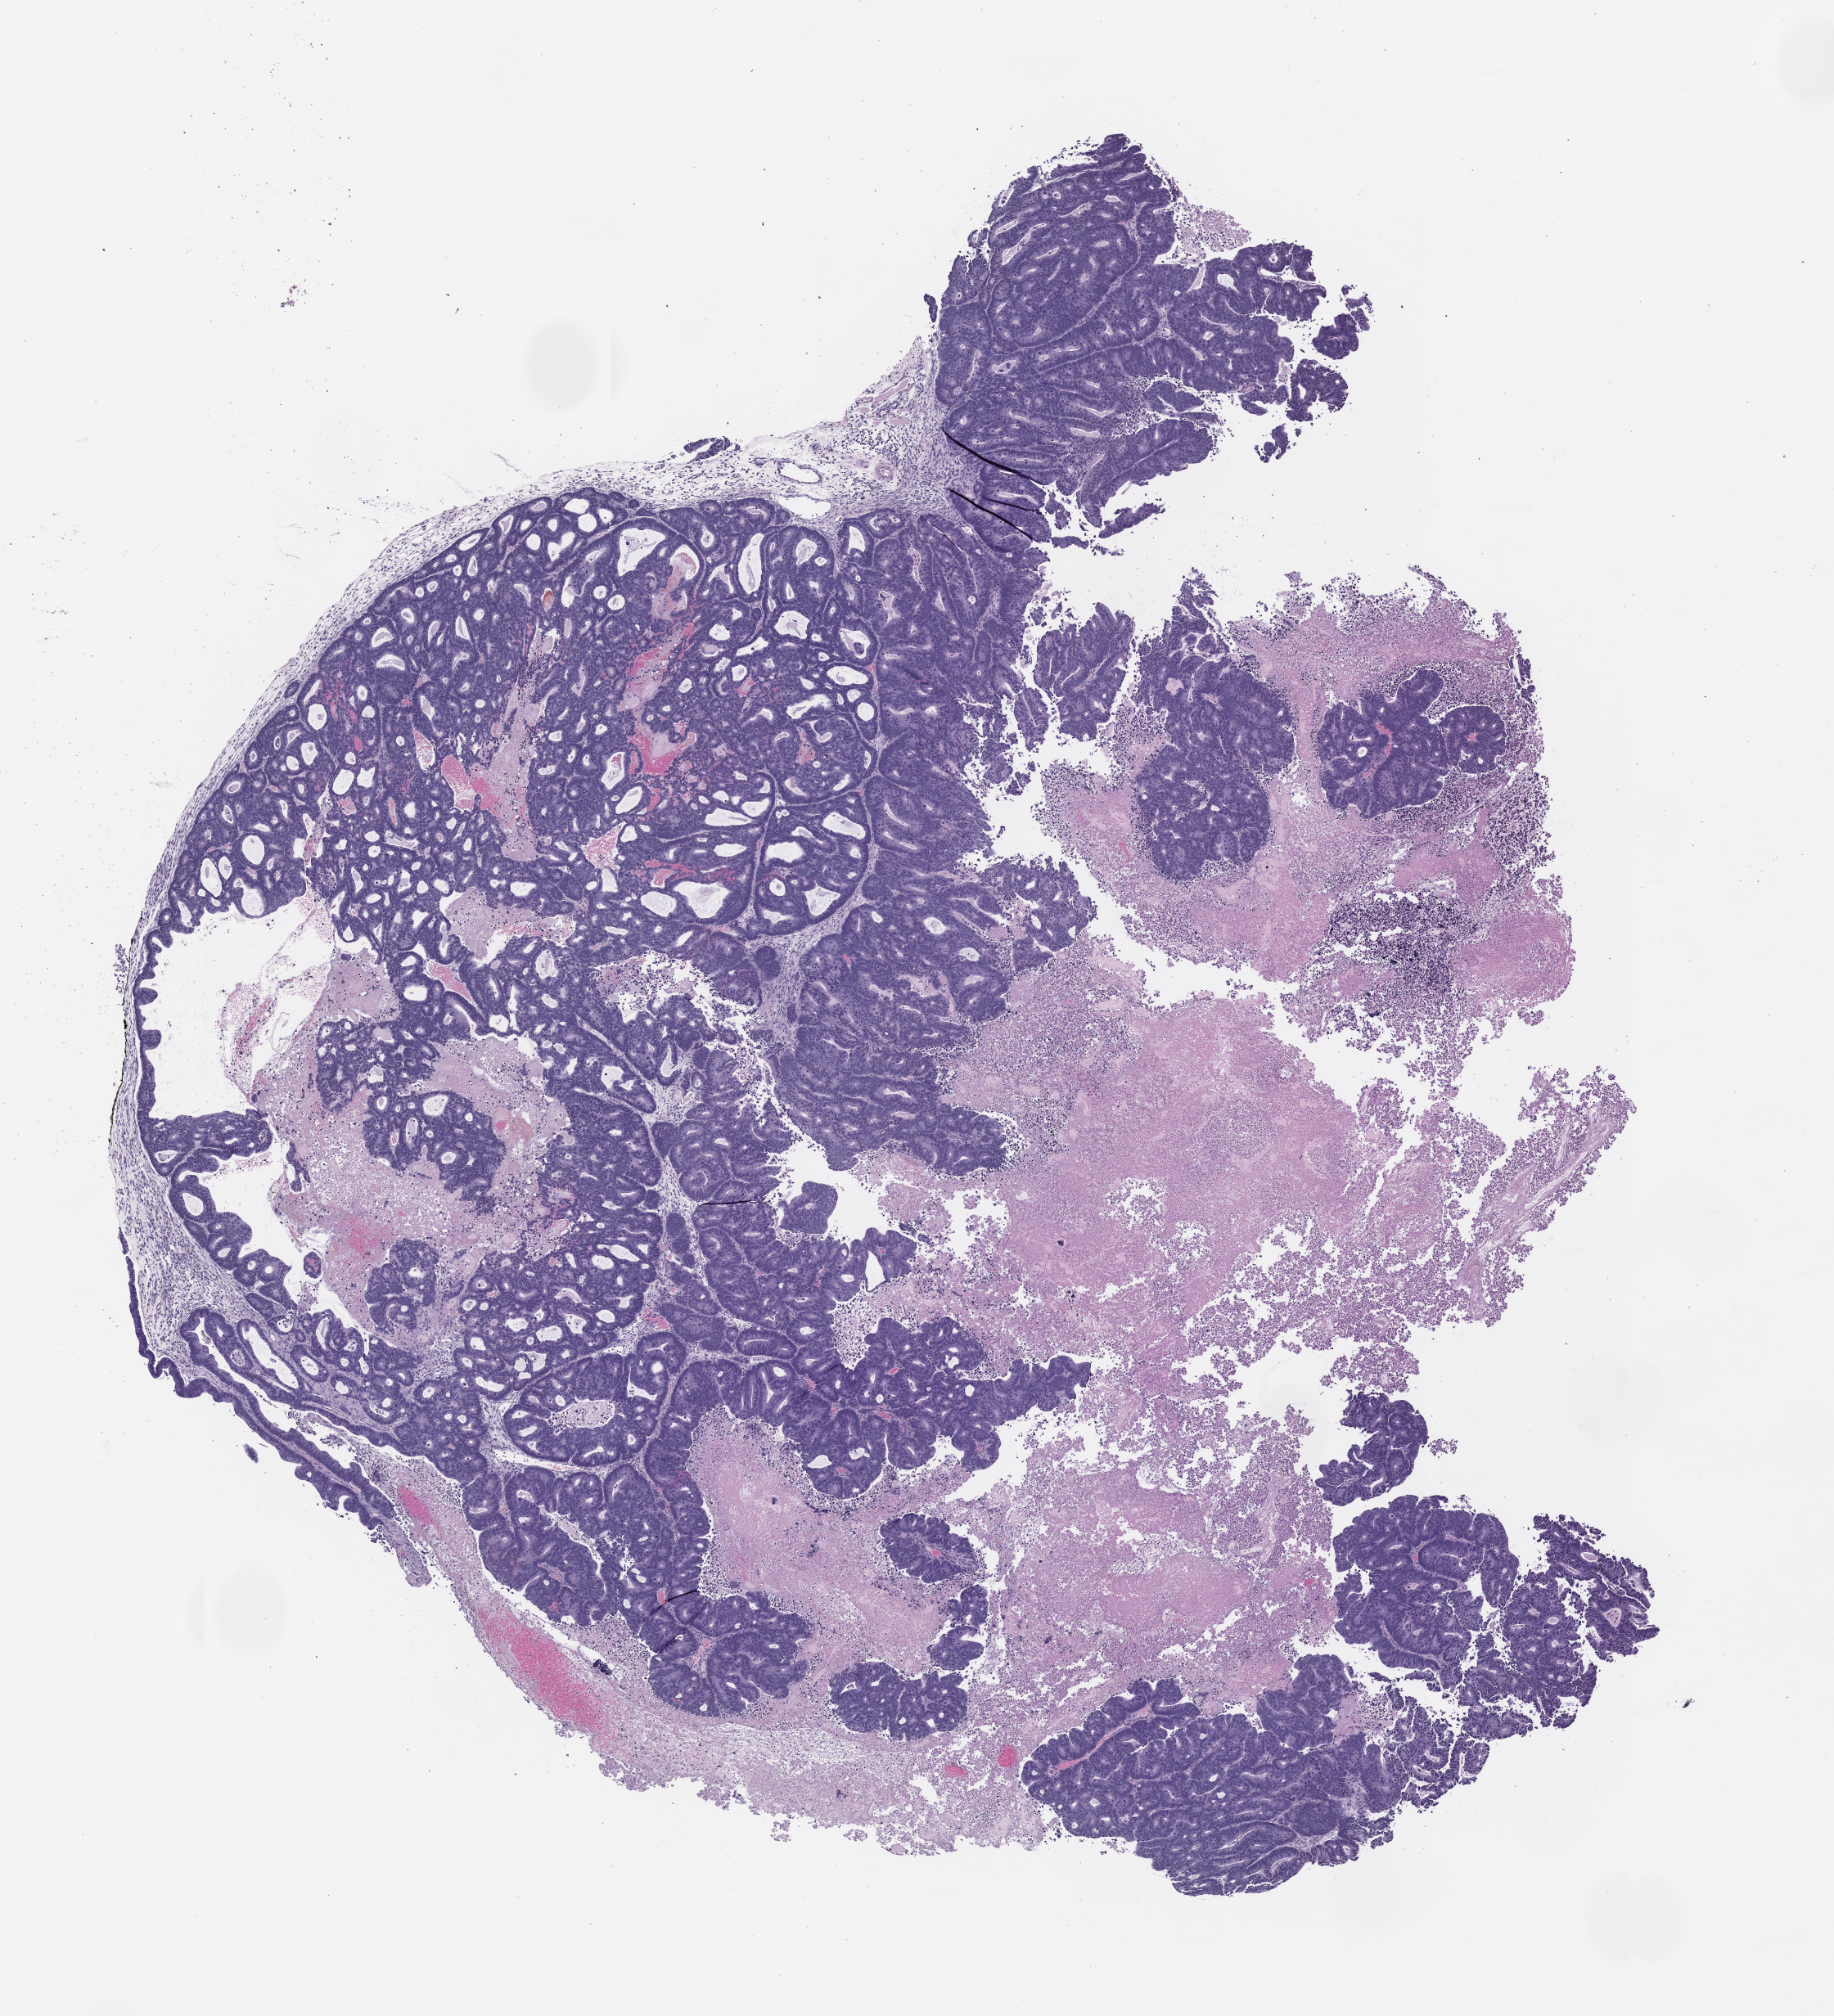
H&E whole-slide image of a patient-derived xenograft (PDX) tumor grown in a mouse, passage 1, low-resolution overview of the scanned area, about 9.0 x 9.9 mm. Formalin-fixed paraffin-embedded section. Originating tumor site category: rectum.
* originating patient diagnosis: Rectal Adenocarcinoma